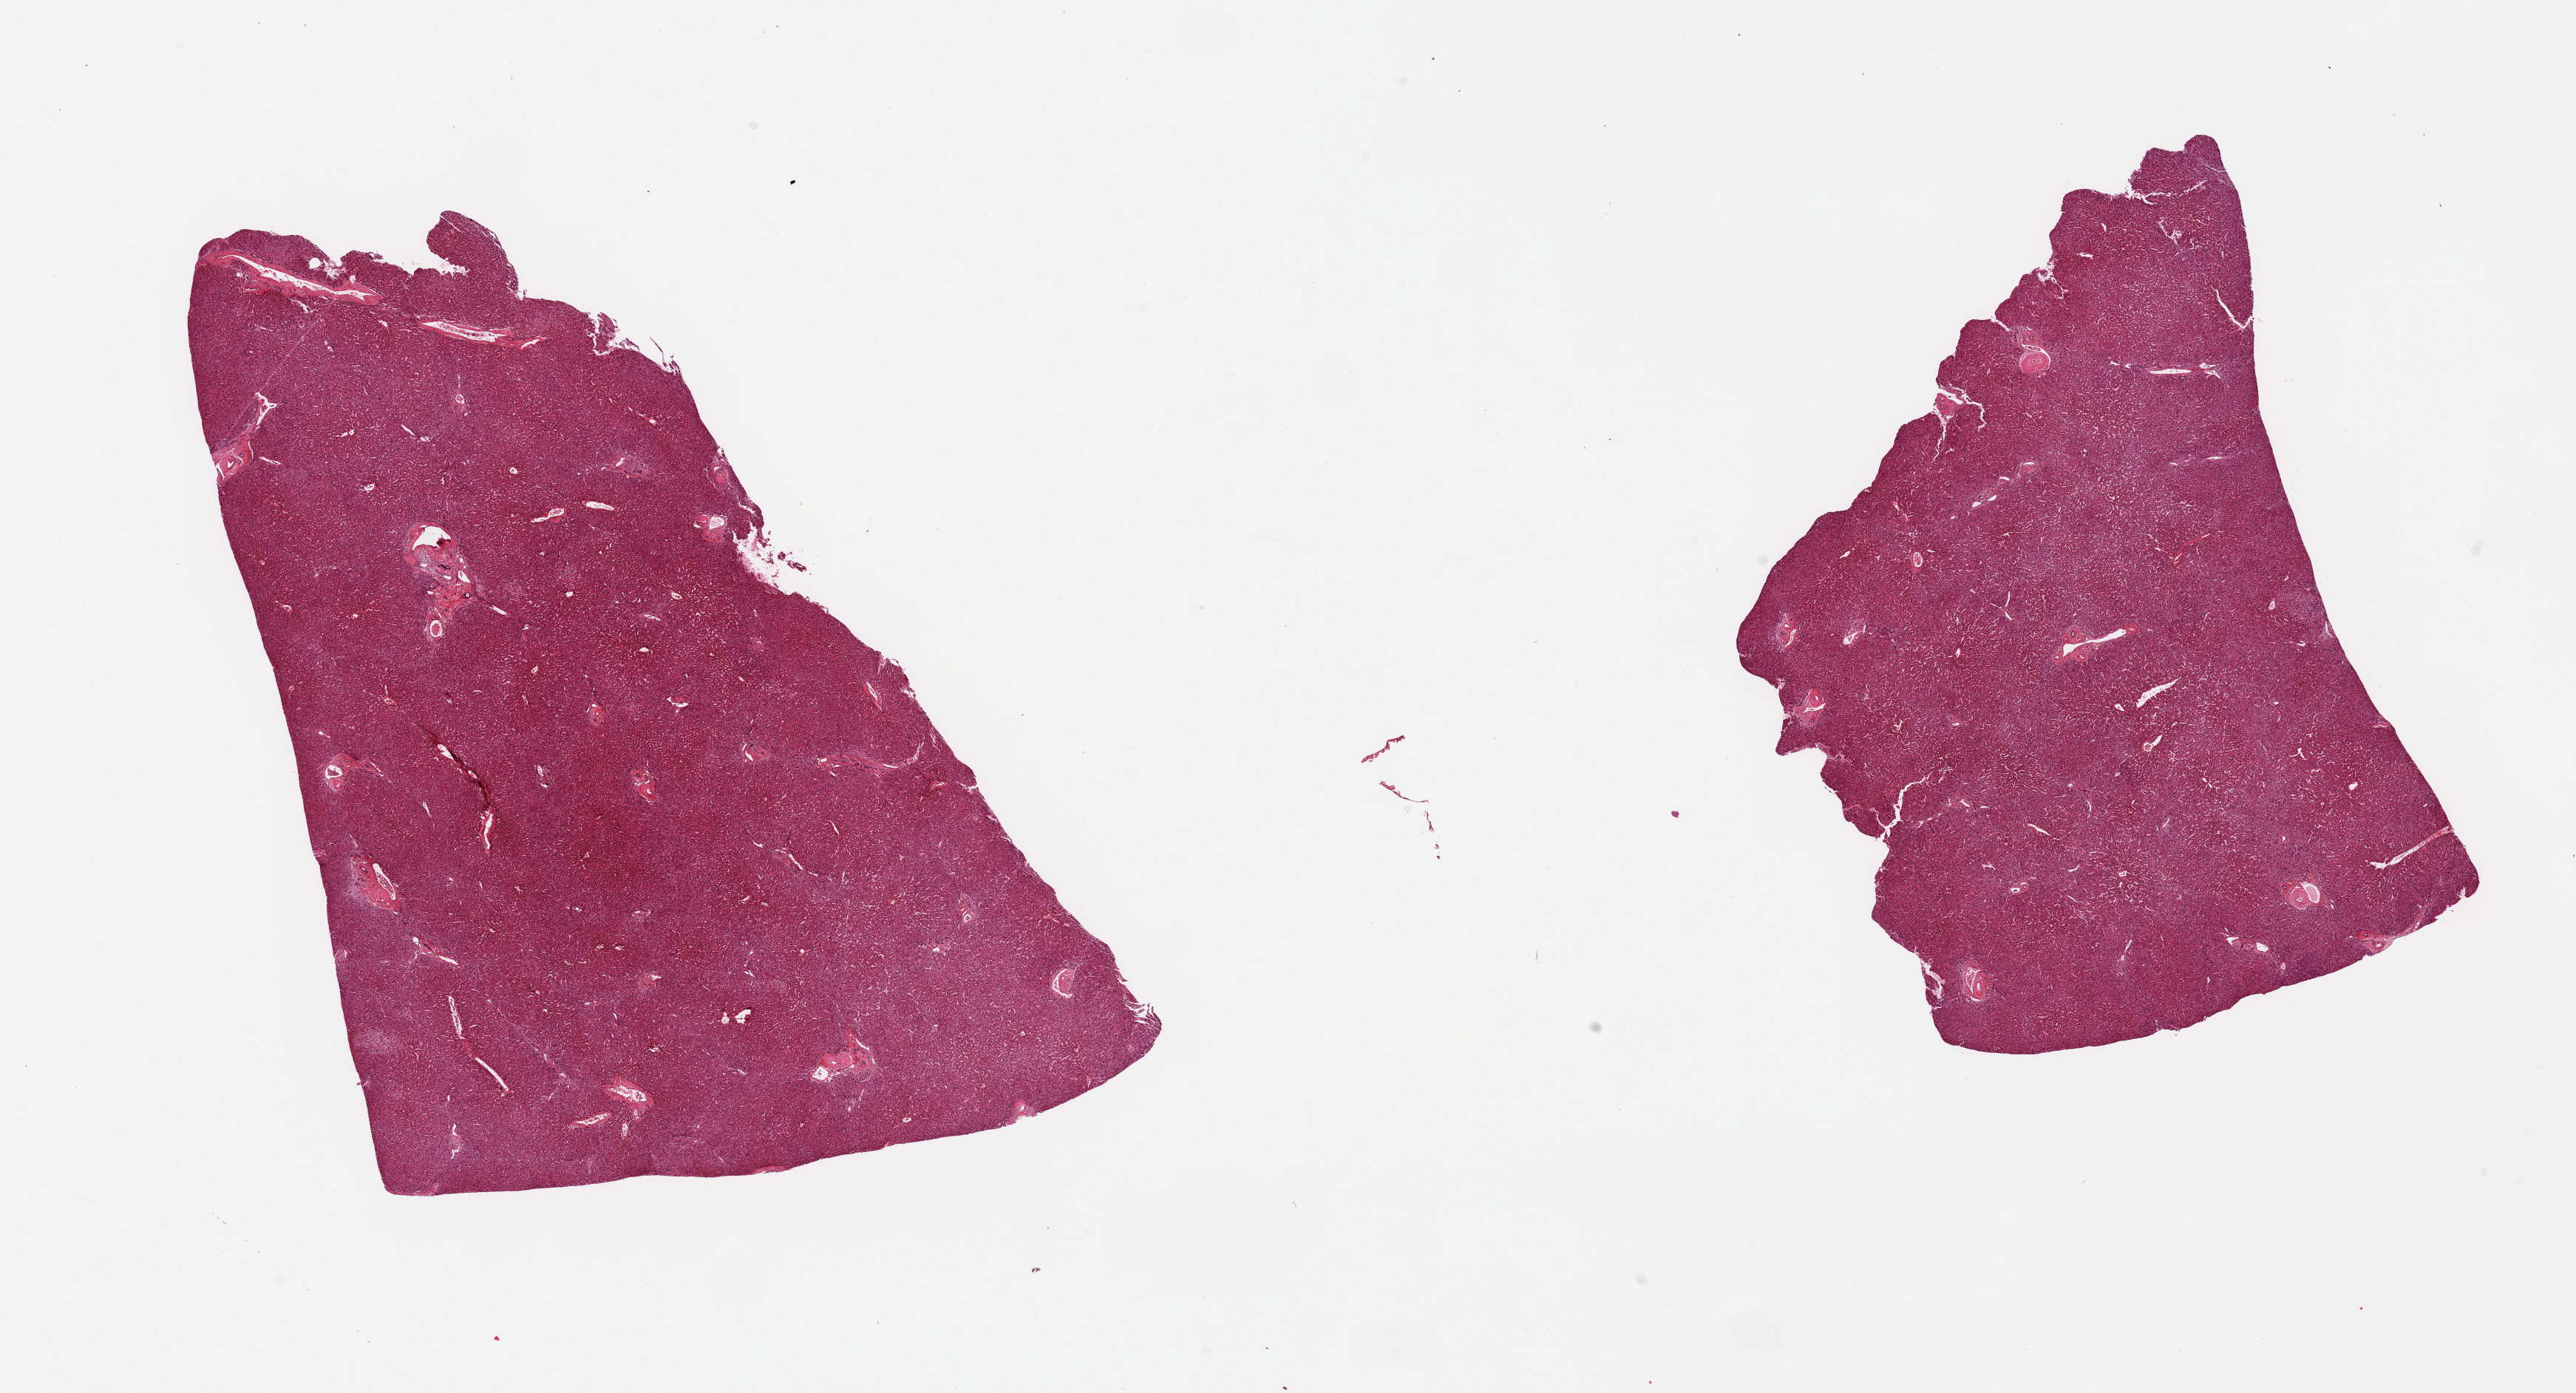
Whole-slide image, hematoxylin and eosin (H&E) stain — a low-resolution overview of the entire scanned area, about 27.6 x 14.9 mm; PAXgene-fixed, paraffin-embedded tissue; sampled site (target tissue): liver; donor tissue sample. Donor sex: female.
Reviewer comment on this tissue sample: 2 pieces; most small portal space arteries have prominent mural sclerosis, otherwise no significant changes; could represent localized amyloid or effect of hypertension.